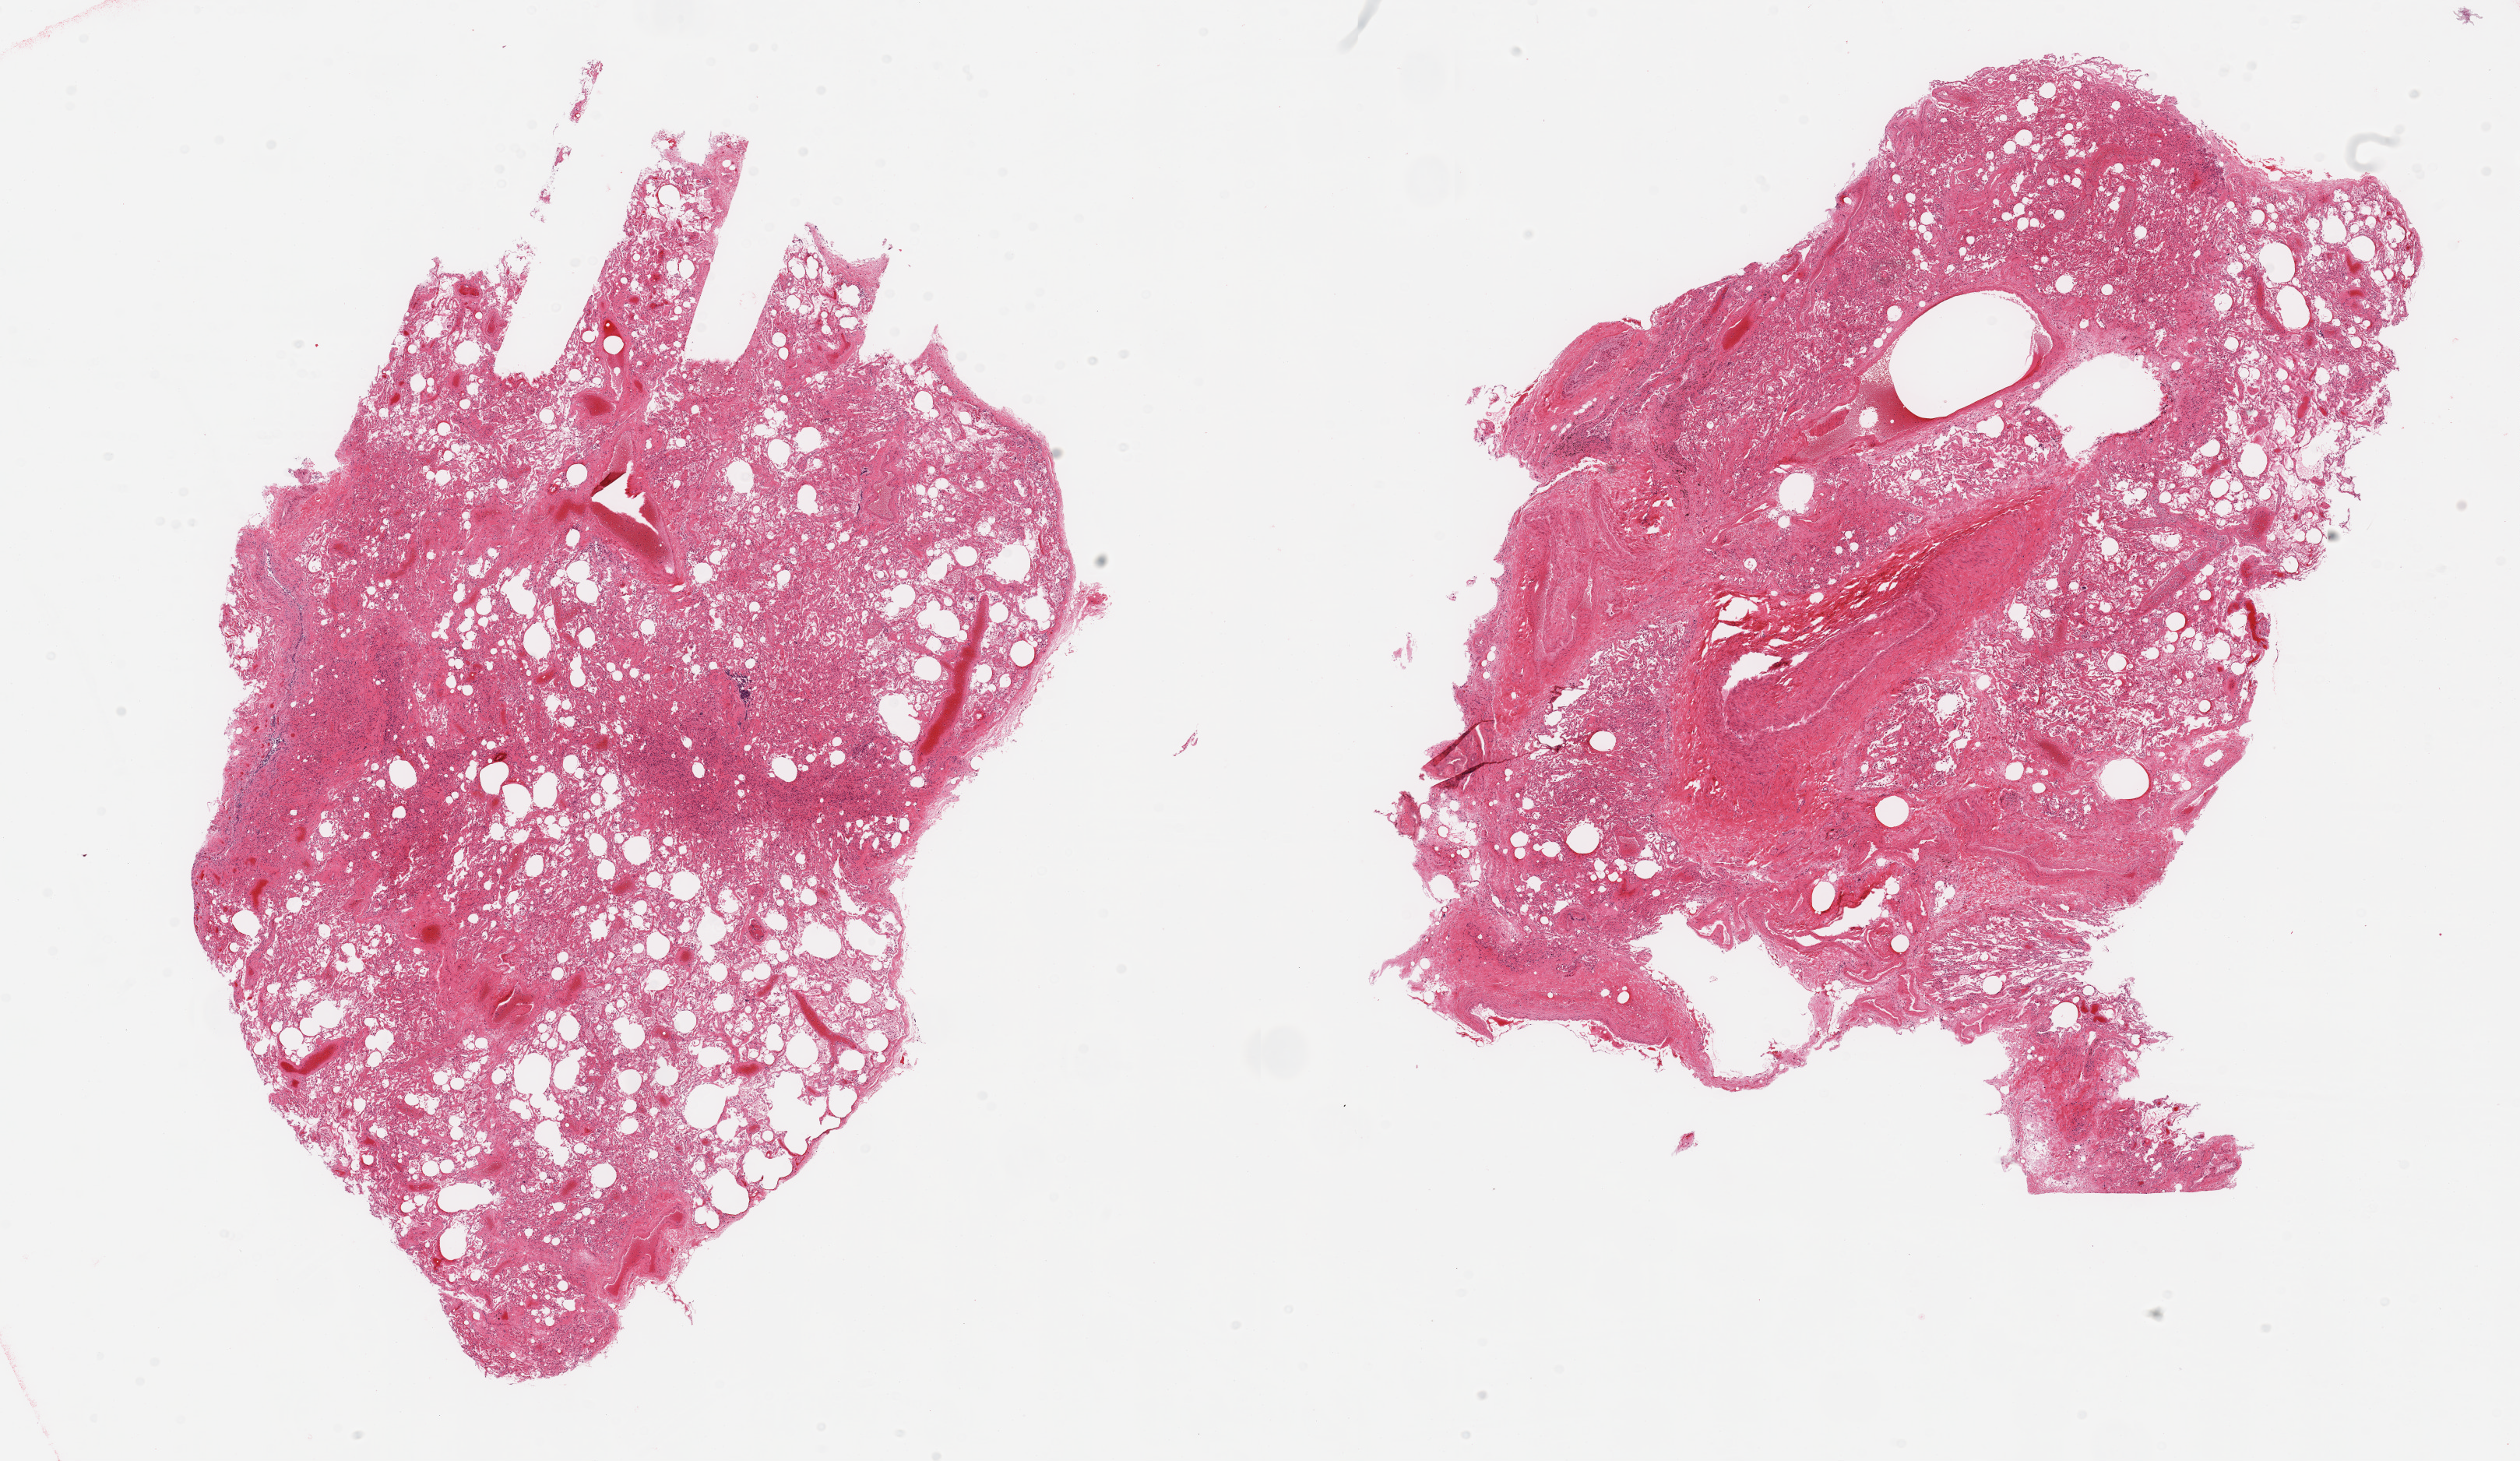
Haematoxylin and eosin whole-slide image — a low-resolution overview of the entire scanned area, about 25.6 x 14.8 mm. PAXgene-fixed paraffin-embedded (PFPE) section. Target tissue: lung. Donor tissue sample. Donor: male.
Reviewer comment on this tissue sample: 2 pieces, moderate congestion/edema.